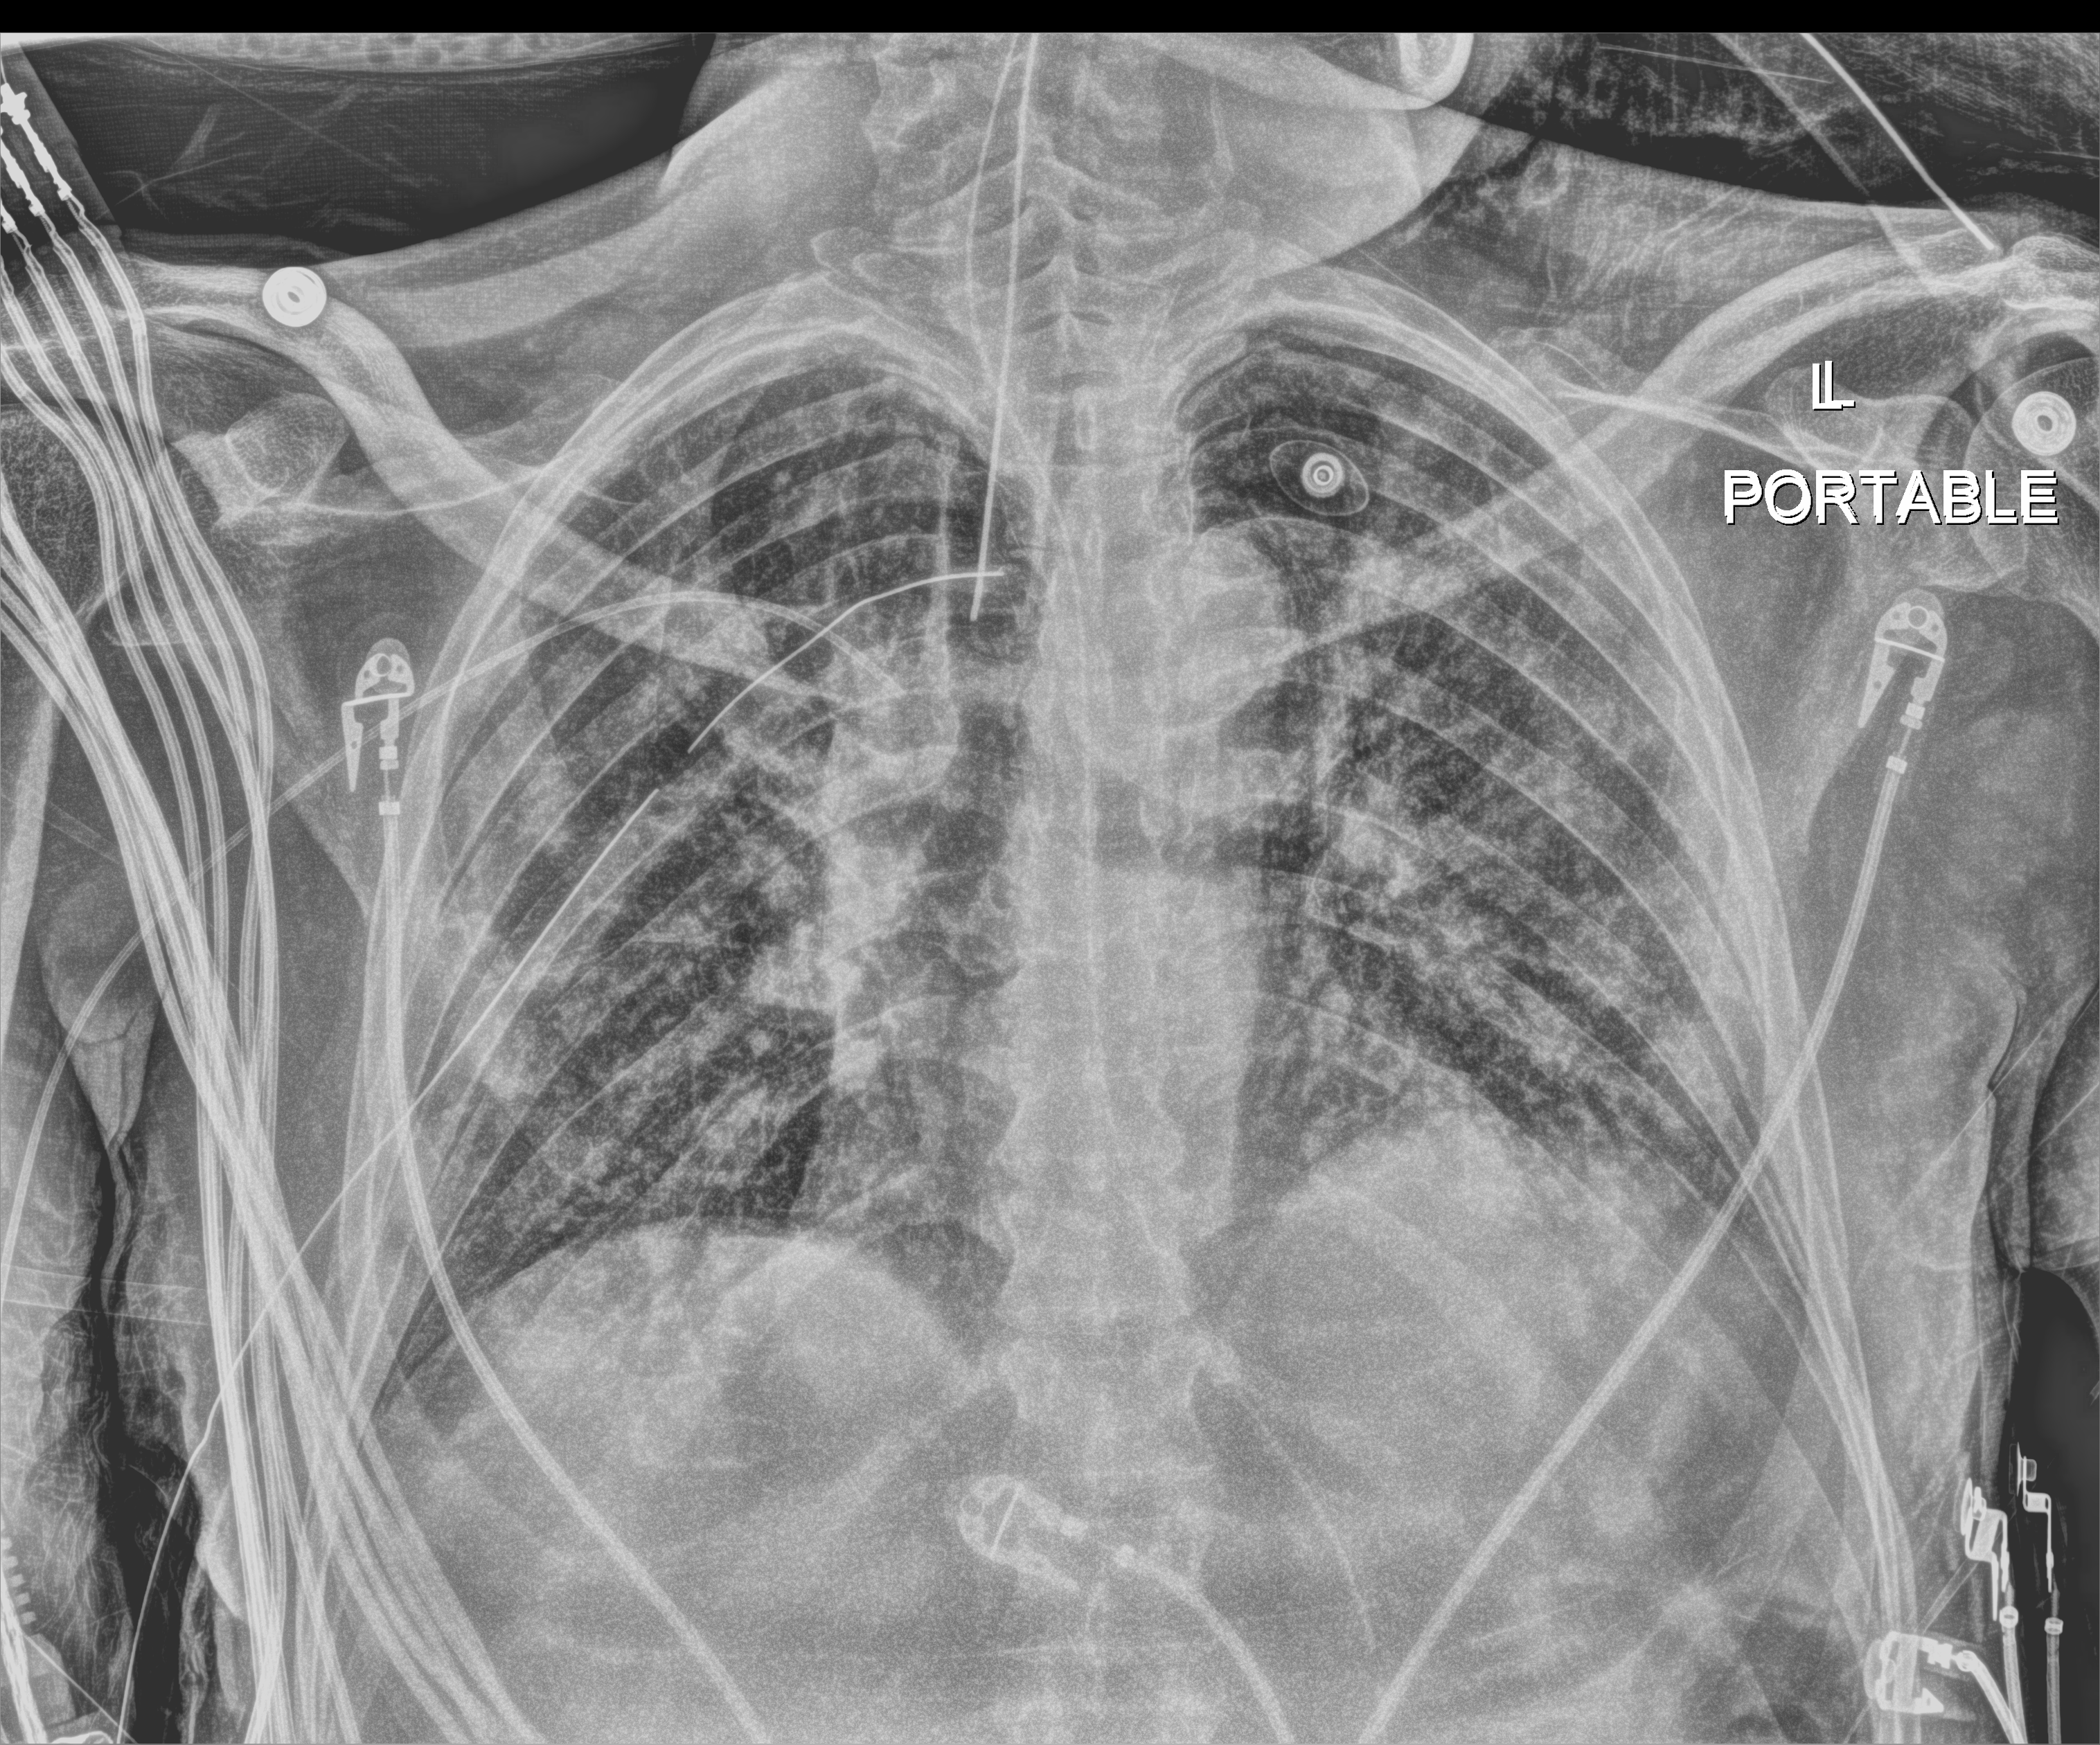
Chest X-ray (portable). Patient hospitalised with COVID-19; male, aged 18–59 years.
From the hospital-stay record, not from the radiograph (when in the stay this image was taken is not recorded): chronic kidney disease (admission record): no; other chronic lung disease (admission record): no.